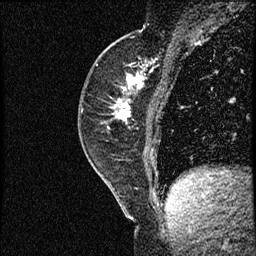
Breast MRI (dynamic contrast-enhanced), one sagittal slice. Slice 26 of 56 in the series (ordered by position). Dynamic contrast-enhanced study with each time point stored as its own series, time point 2 of 3 at this slice position (early post-contrast, ordered by acquisition time). 1.5 T. TE 4.2 ms, TR 17.3 ms. 2 mm slice thickness. 256 × 256 image matrix, field of view 200 × 200 mm. Female patient. Case-level facts recorded for this patient, not image findings: setting: breast cancer imaged before/during neoadjuvant chemotherapy; receptor status: HER2-positive.
Annotated regions visible in this slice (semi-automatic segmentation, software-assisted and operator-edited):
- analysis volume of interest (the breast-tissue region the enhancement analysis was run in; not a lesion): box from (x=78, y=50) to (x=156, y=155) px
- tumour enhancement mask (voxels above the 100 % enhancement threshold inside the analysis volume of interest): (x=114, y=75)–(x=144, y=120)